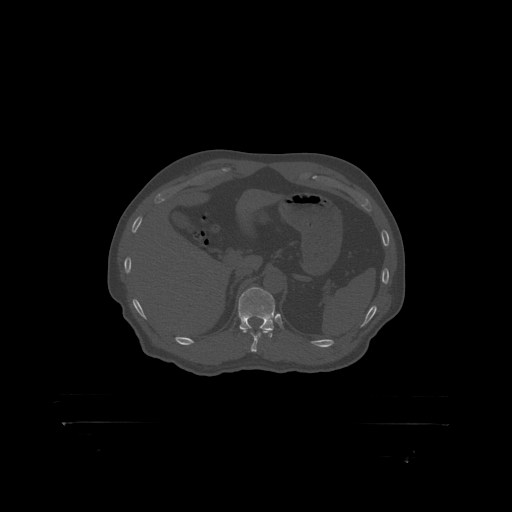
CT including the spine, one axial slice. Slice 364 of 399 in the series (ordered by position). Bone window (W 1800 / L 400 HU). 1.25 mm slice thickness. 512 × 512 image matrix. Patient: male, 46 years. From the clinical record (not read from this slice): primary cancer: skin.
Annotated regions visible in this slice (semi-automatic segmentation, software-assisted and operator-edited):
- T12 vertebra: bounding box <239,287,280,319> (left, top, right, bottom; pixels)